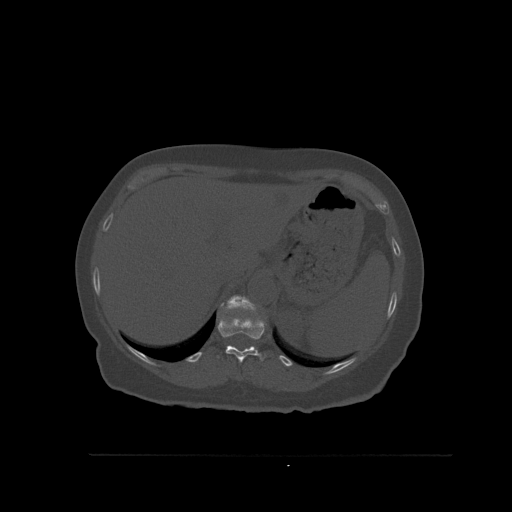
CT including the spine, one axial slice; slice 301 of 527 in the series (ordered by position); bone window (W 1800 / L 400 HU); 1.5 mm slice thickness; 512 × 512 image matrix, field of view 470 × 470 mm. Patient: female, 73 years. From the clinical record (not read from this slice): primary cancer: breast; vertebrae with lytic lesions (as recorded): L2.
Annotated regions visible in this slice (semi-automatic segmentation, software-assisted and operator-edited):
- T11 vertebra: bounding box (x1, y1, x2, y2) in pixels: (217, 316, 266, 363)
- T12 vertebra: (220, 295, 258, 315)